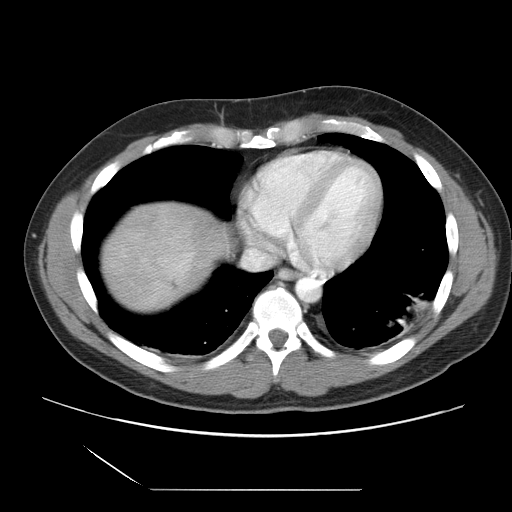
Contrast-enhanced abdominal CT, one axial slice. Slice 32 of 39 in the series (ordered by position). 120 kVp. Soft-tissue window (W 400 / L 40 HU). 5 mm slice thickness. 512 × 512 image matrix, field of view 395 × 395 mm. Male patient, age 39 years. Case-level facts recorded for this patient, not image findings: diagnosis: colorectal cancer liver metastases, imaged before liver resection; multiple liver metastases: yes; largest metastasis: 1.3 cm; disease in both lobes: no.
Outlined on this slice (expert manual segmentation):
- liver: bounding box (x1, y1, x2, y2) in pixels: (99, 201, 226, 313)
- planned liver remnant (the part of the liver to remain after resection): (186, 207, 210, 219)
- liver metastasis: (169, 282, 177, 289)